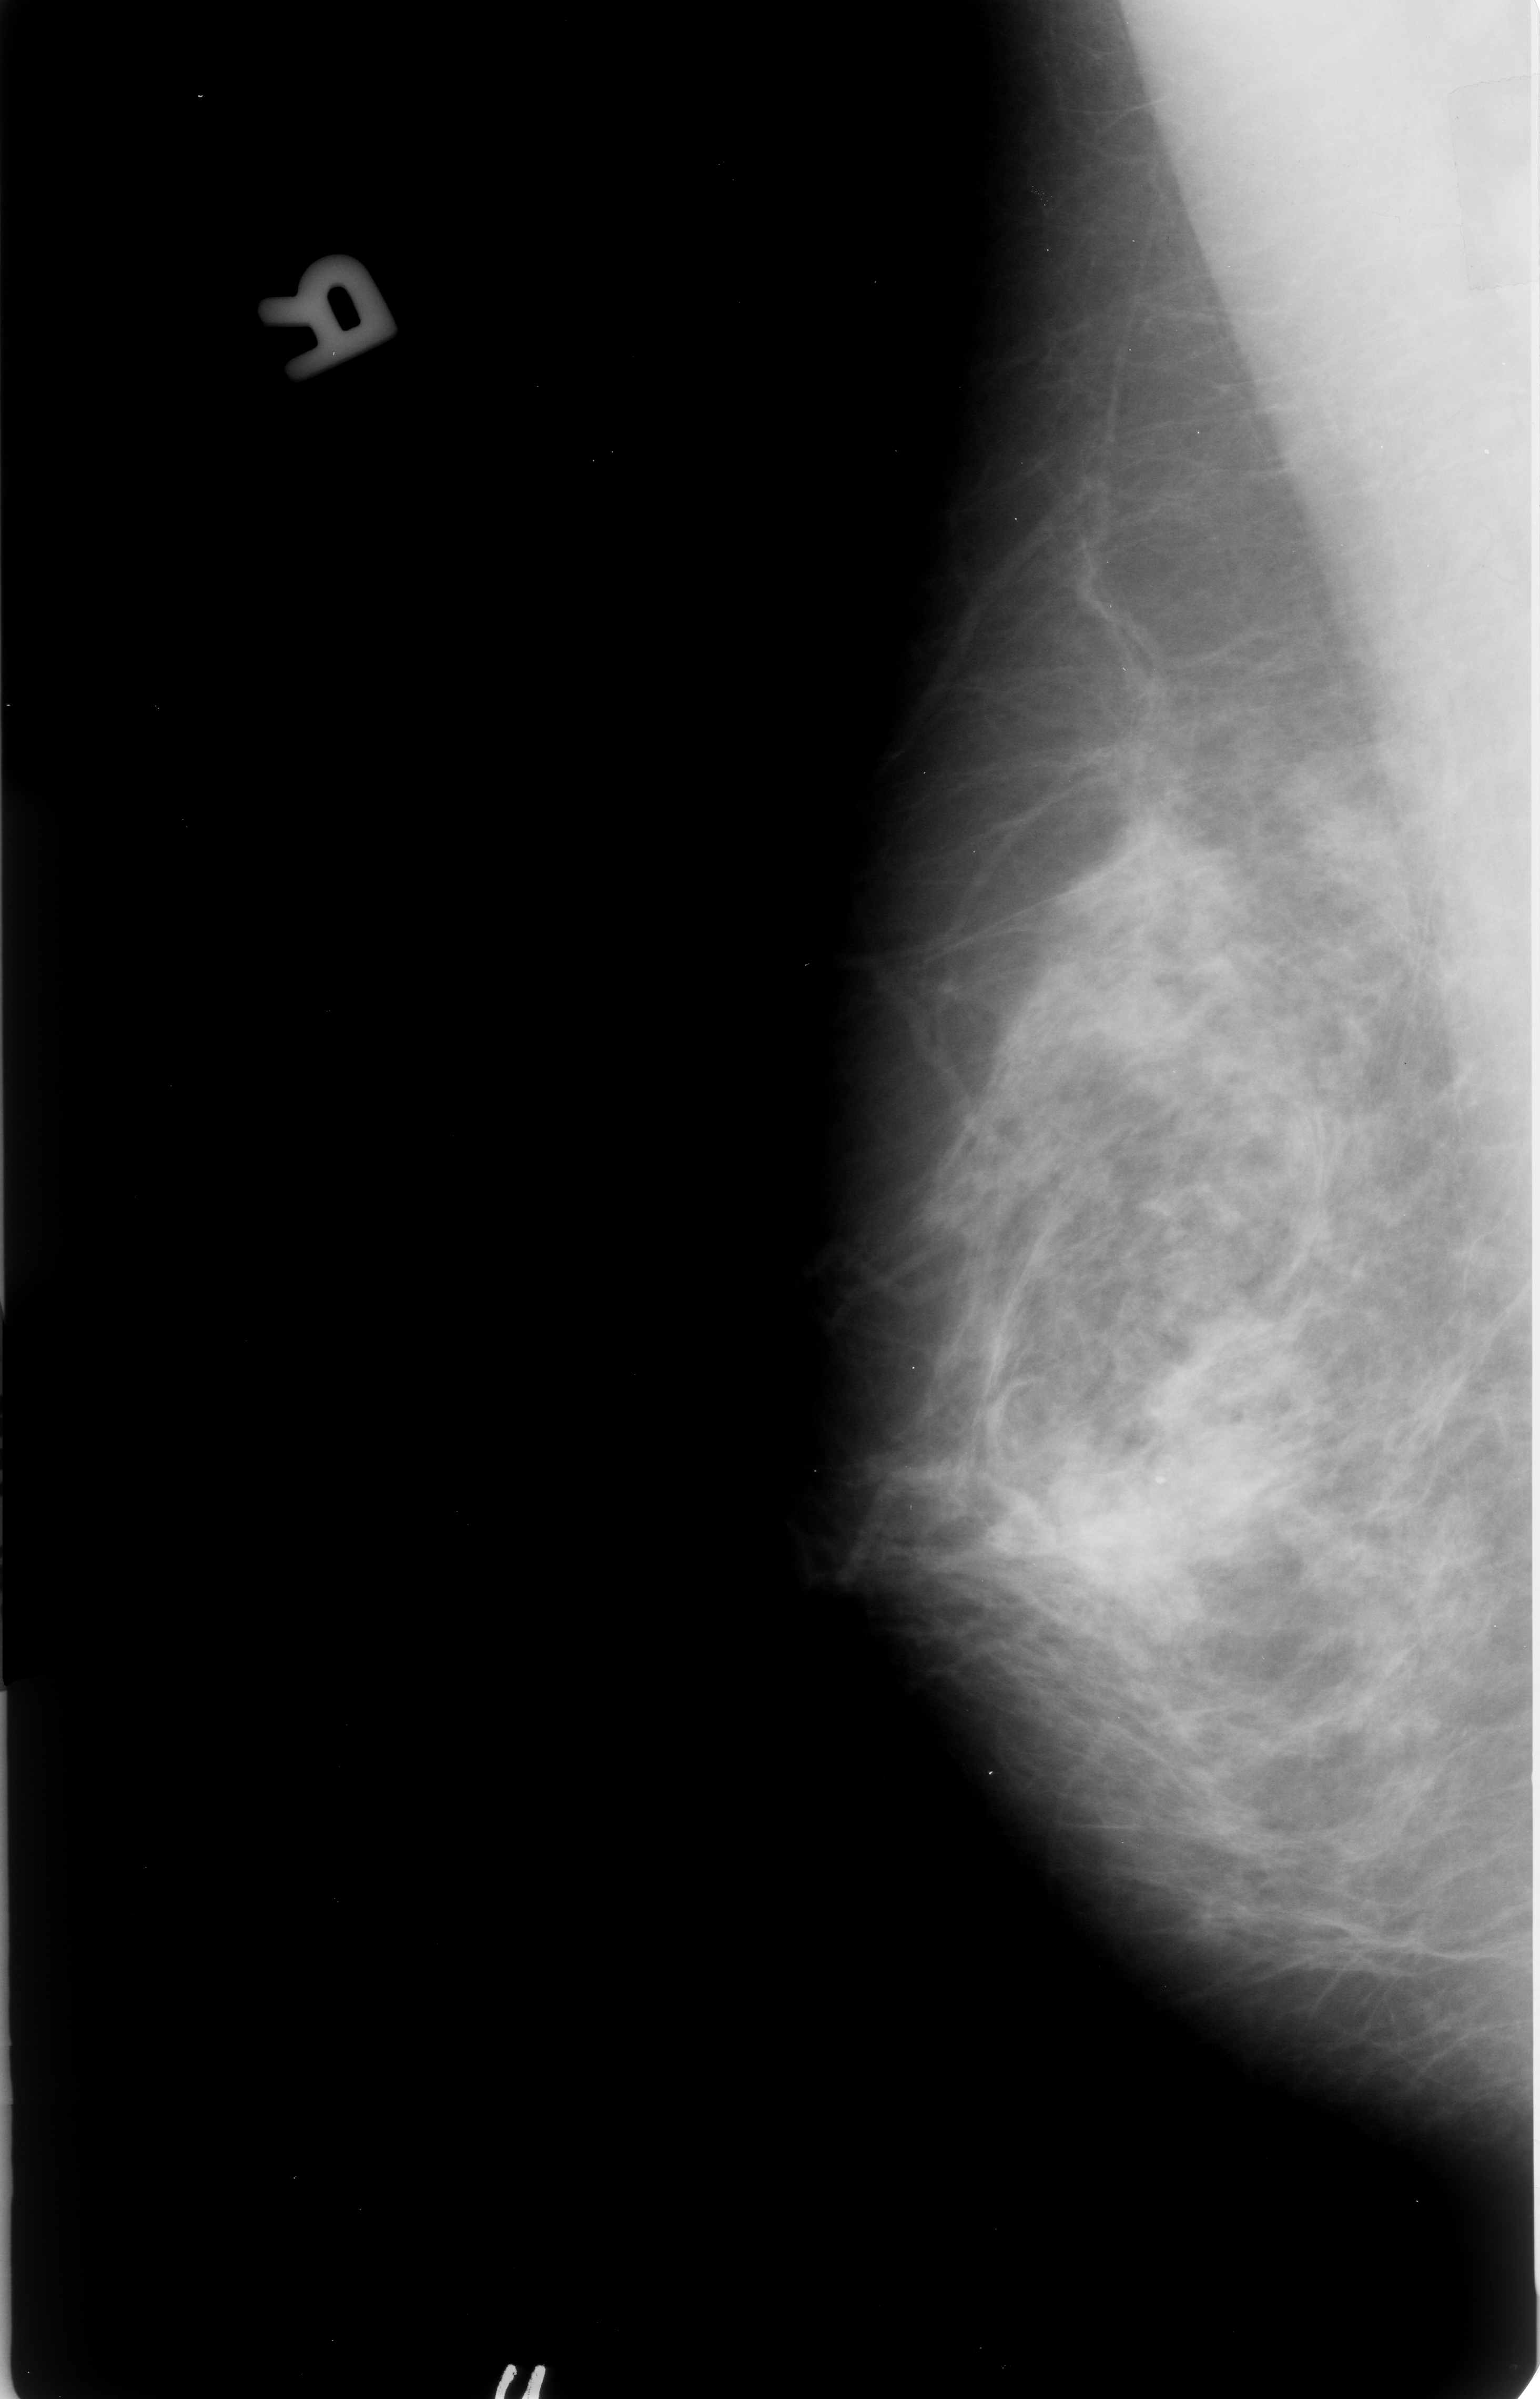
Mammogram (digitized film); right breast; mediolateral oblique (MLO) view.
- Calcifications, morphology pleomorphic, distribution clustered; BI-RADS assessment category 3; subtlety rating 2 on a 1 (subtle) to 5 (obvious) scale; pathology (as recorded): malignant.